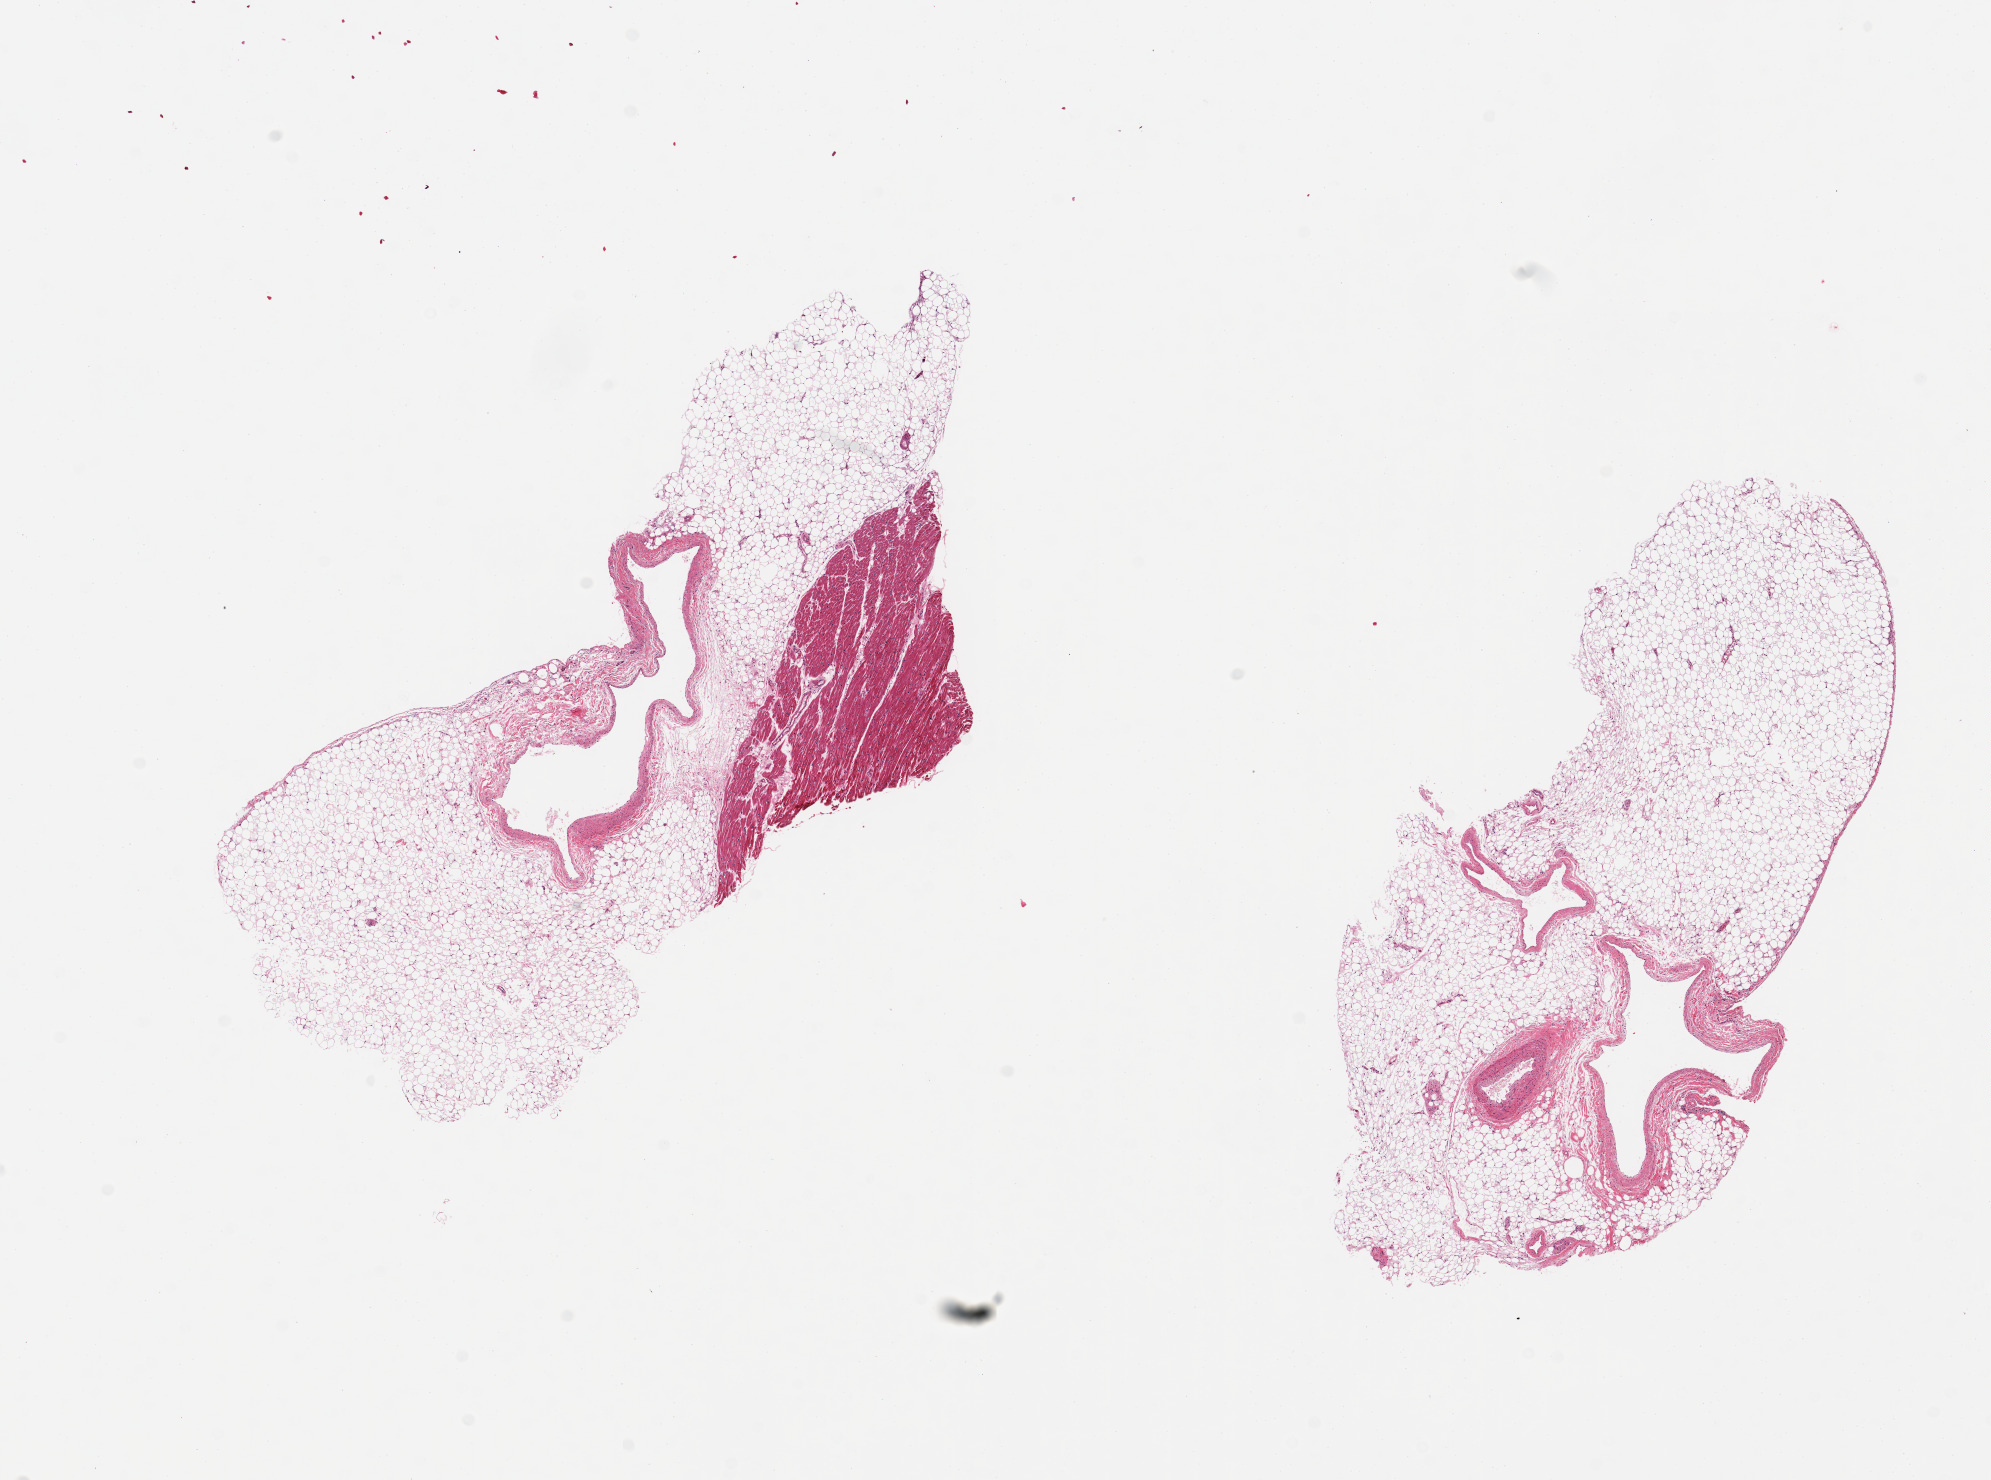
Whole-slide image, hematoxylin and eosin (H&E) stain, a low-resolution overview of the entire scanned area, about 15.8 x 11.7 mm. PAXgene-fixed, paraffin-embedded tissue. Sampled site (target tissue): coronary artery. Donor tissue sample. Donor sex: female.
Reviewer comment on this tissue sample: 2 pieces; 1 piece contains a vein, myocardium and fat; other is largely fat with veins and a small <1mm artery [all labeled].